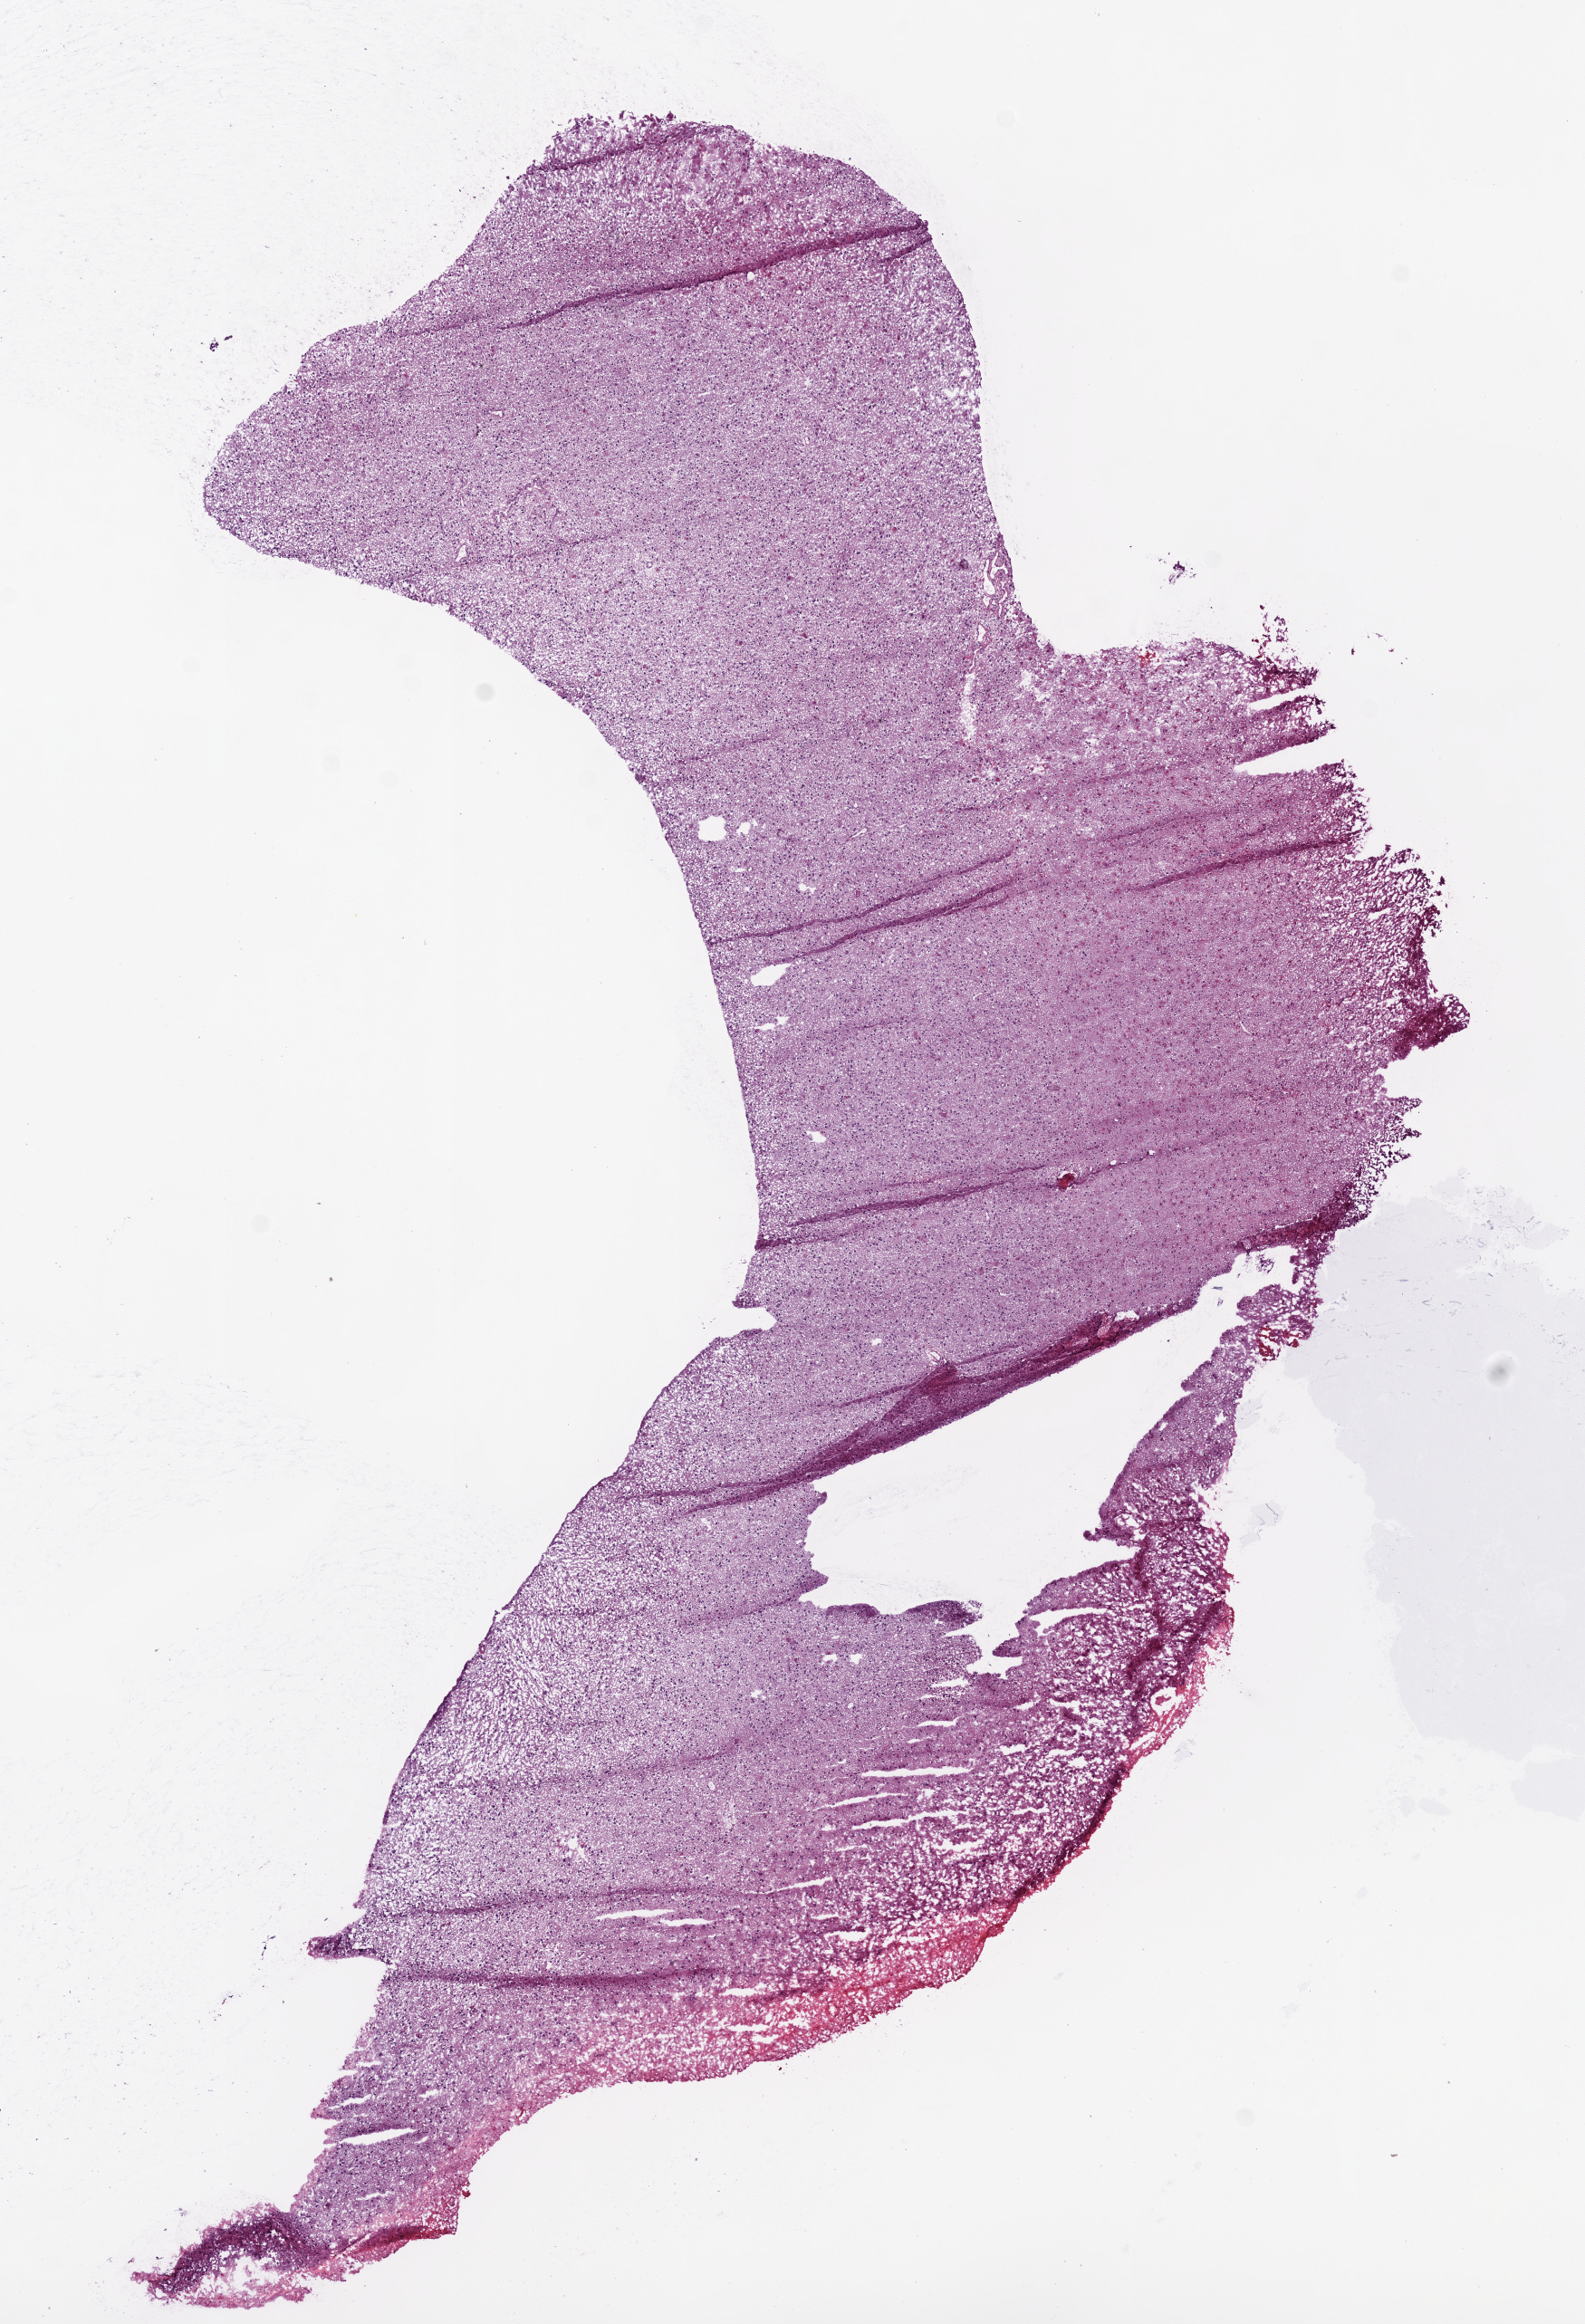
H&E whole-slide image — a low-resolution overview of the entire scanned area, about 7.0 x 10.3 mm (from a 20x scan), frozen section, primary tumour sample from the brain. Female patient; age at initial diagnosis 63 years. Composition of this section per pathologist review: tumour cells 100%, tumour nuclei 80%, normal cells 0%, stromal cells 0%, necrosis 0%.
Pathologic diagnosis: Glioblastoma.